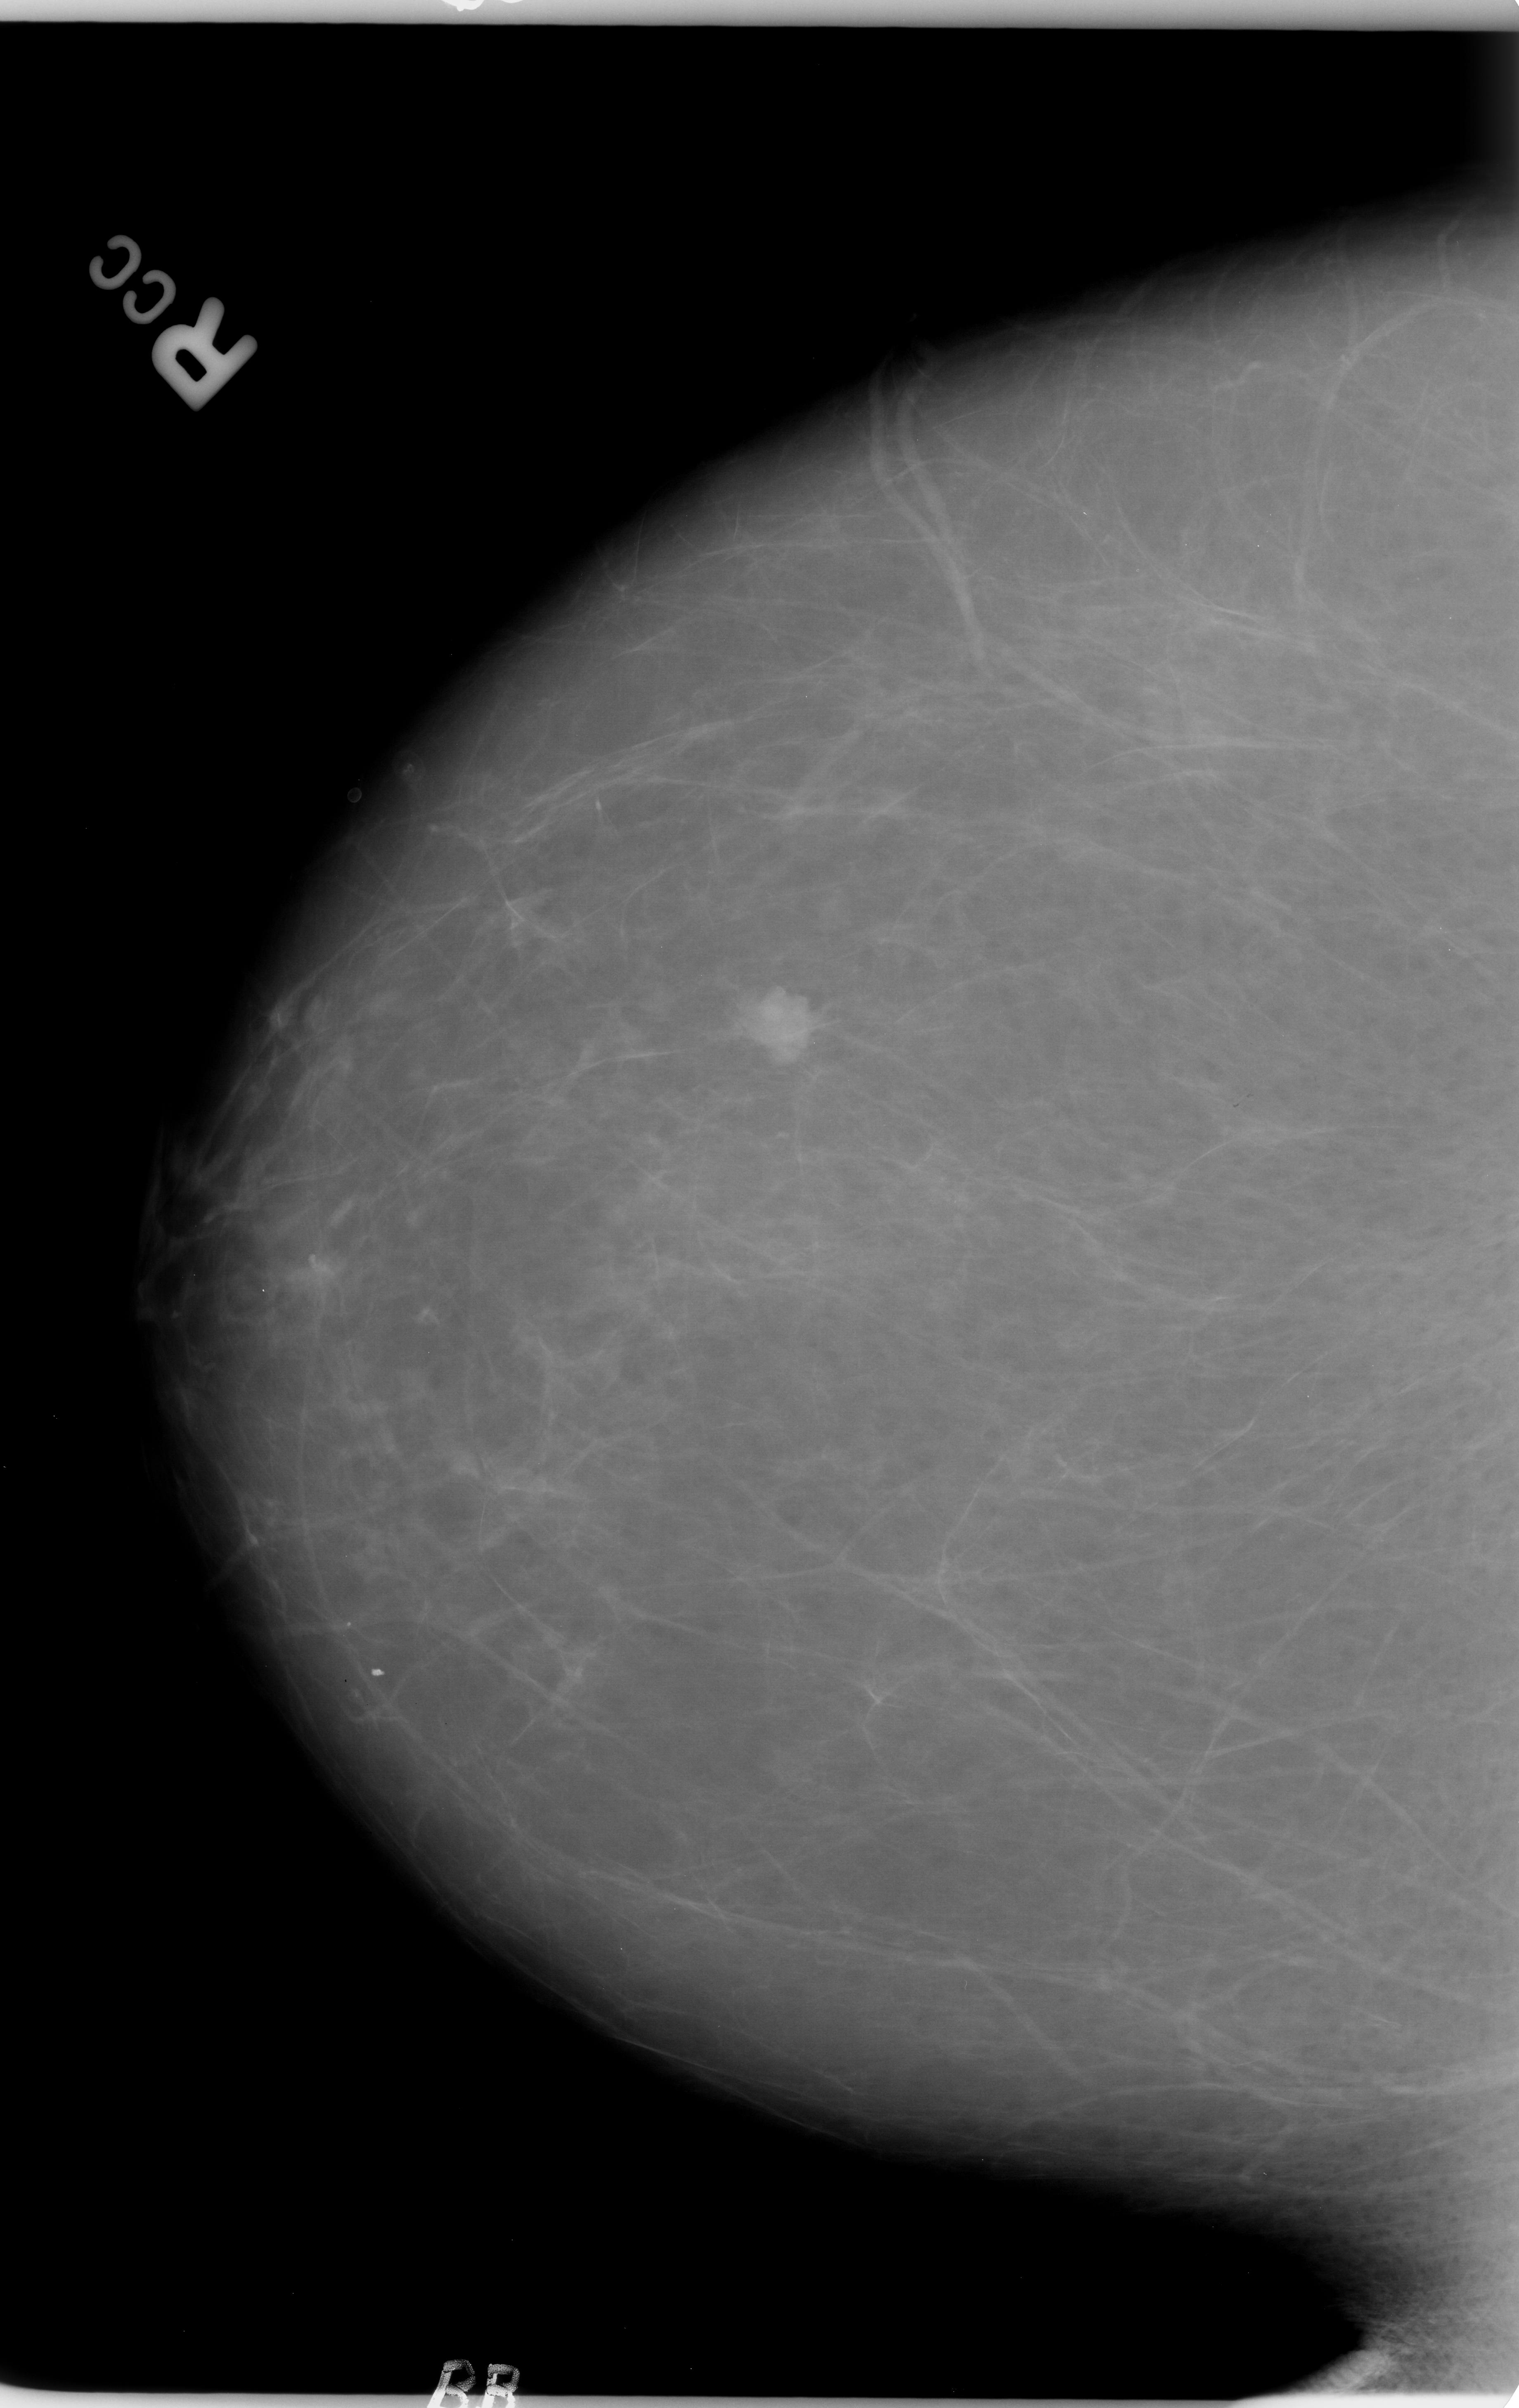
Scanned film-screen mammogram; right breast; craniocaudal (CC) view; BI-RADS breast density category 1 (scale 1–4); 1519 × 2408 image matrix.
Marked abnormalities (boxes around the expert regions of interest):
- mass, shape lobulated, margins circumscribed / ill defined; BI-RADS assessment category 4; pathology result (as recorded, not read from the image): benign: bounding box [x1, y1, x2, y2] px = [734, 985, 814, 1062]